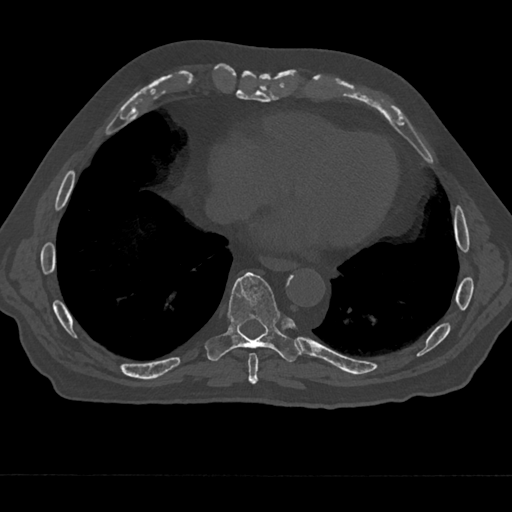
CT including the spine, one axial slice; slice 272 of 797 in the series (ordered by position); reconstruction kernel Br40s/3; bone window (W 1800 / L 400 HU); 0.5 mm slice thickness; 512 × 512 image matrix, field of view 377 × 377 mm. Male patient, age 75 years. From the clinical record (not read from this slice): primary cancer: renal; vertebrae with lytic lesions (as recorded): T4.
Annotated regions visible in this slice (semi-automatic segmentation, software-assisted and operator-edited):
- T8 vertebra: bounding box [x1, y1, x2, y2] px = [248, 353, 259, 385]
- T9 vertebra: [204, 272, 301, 362]